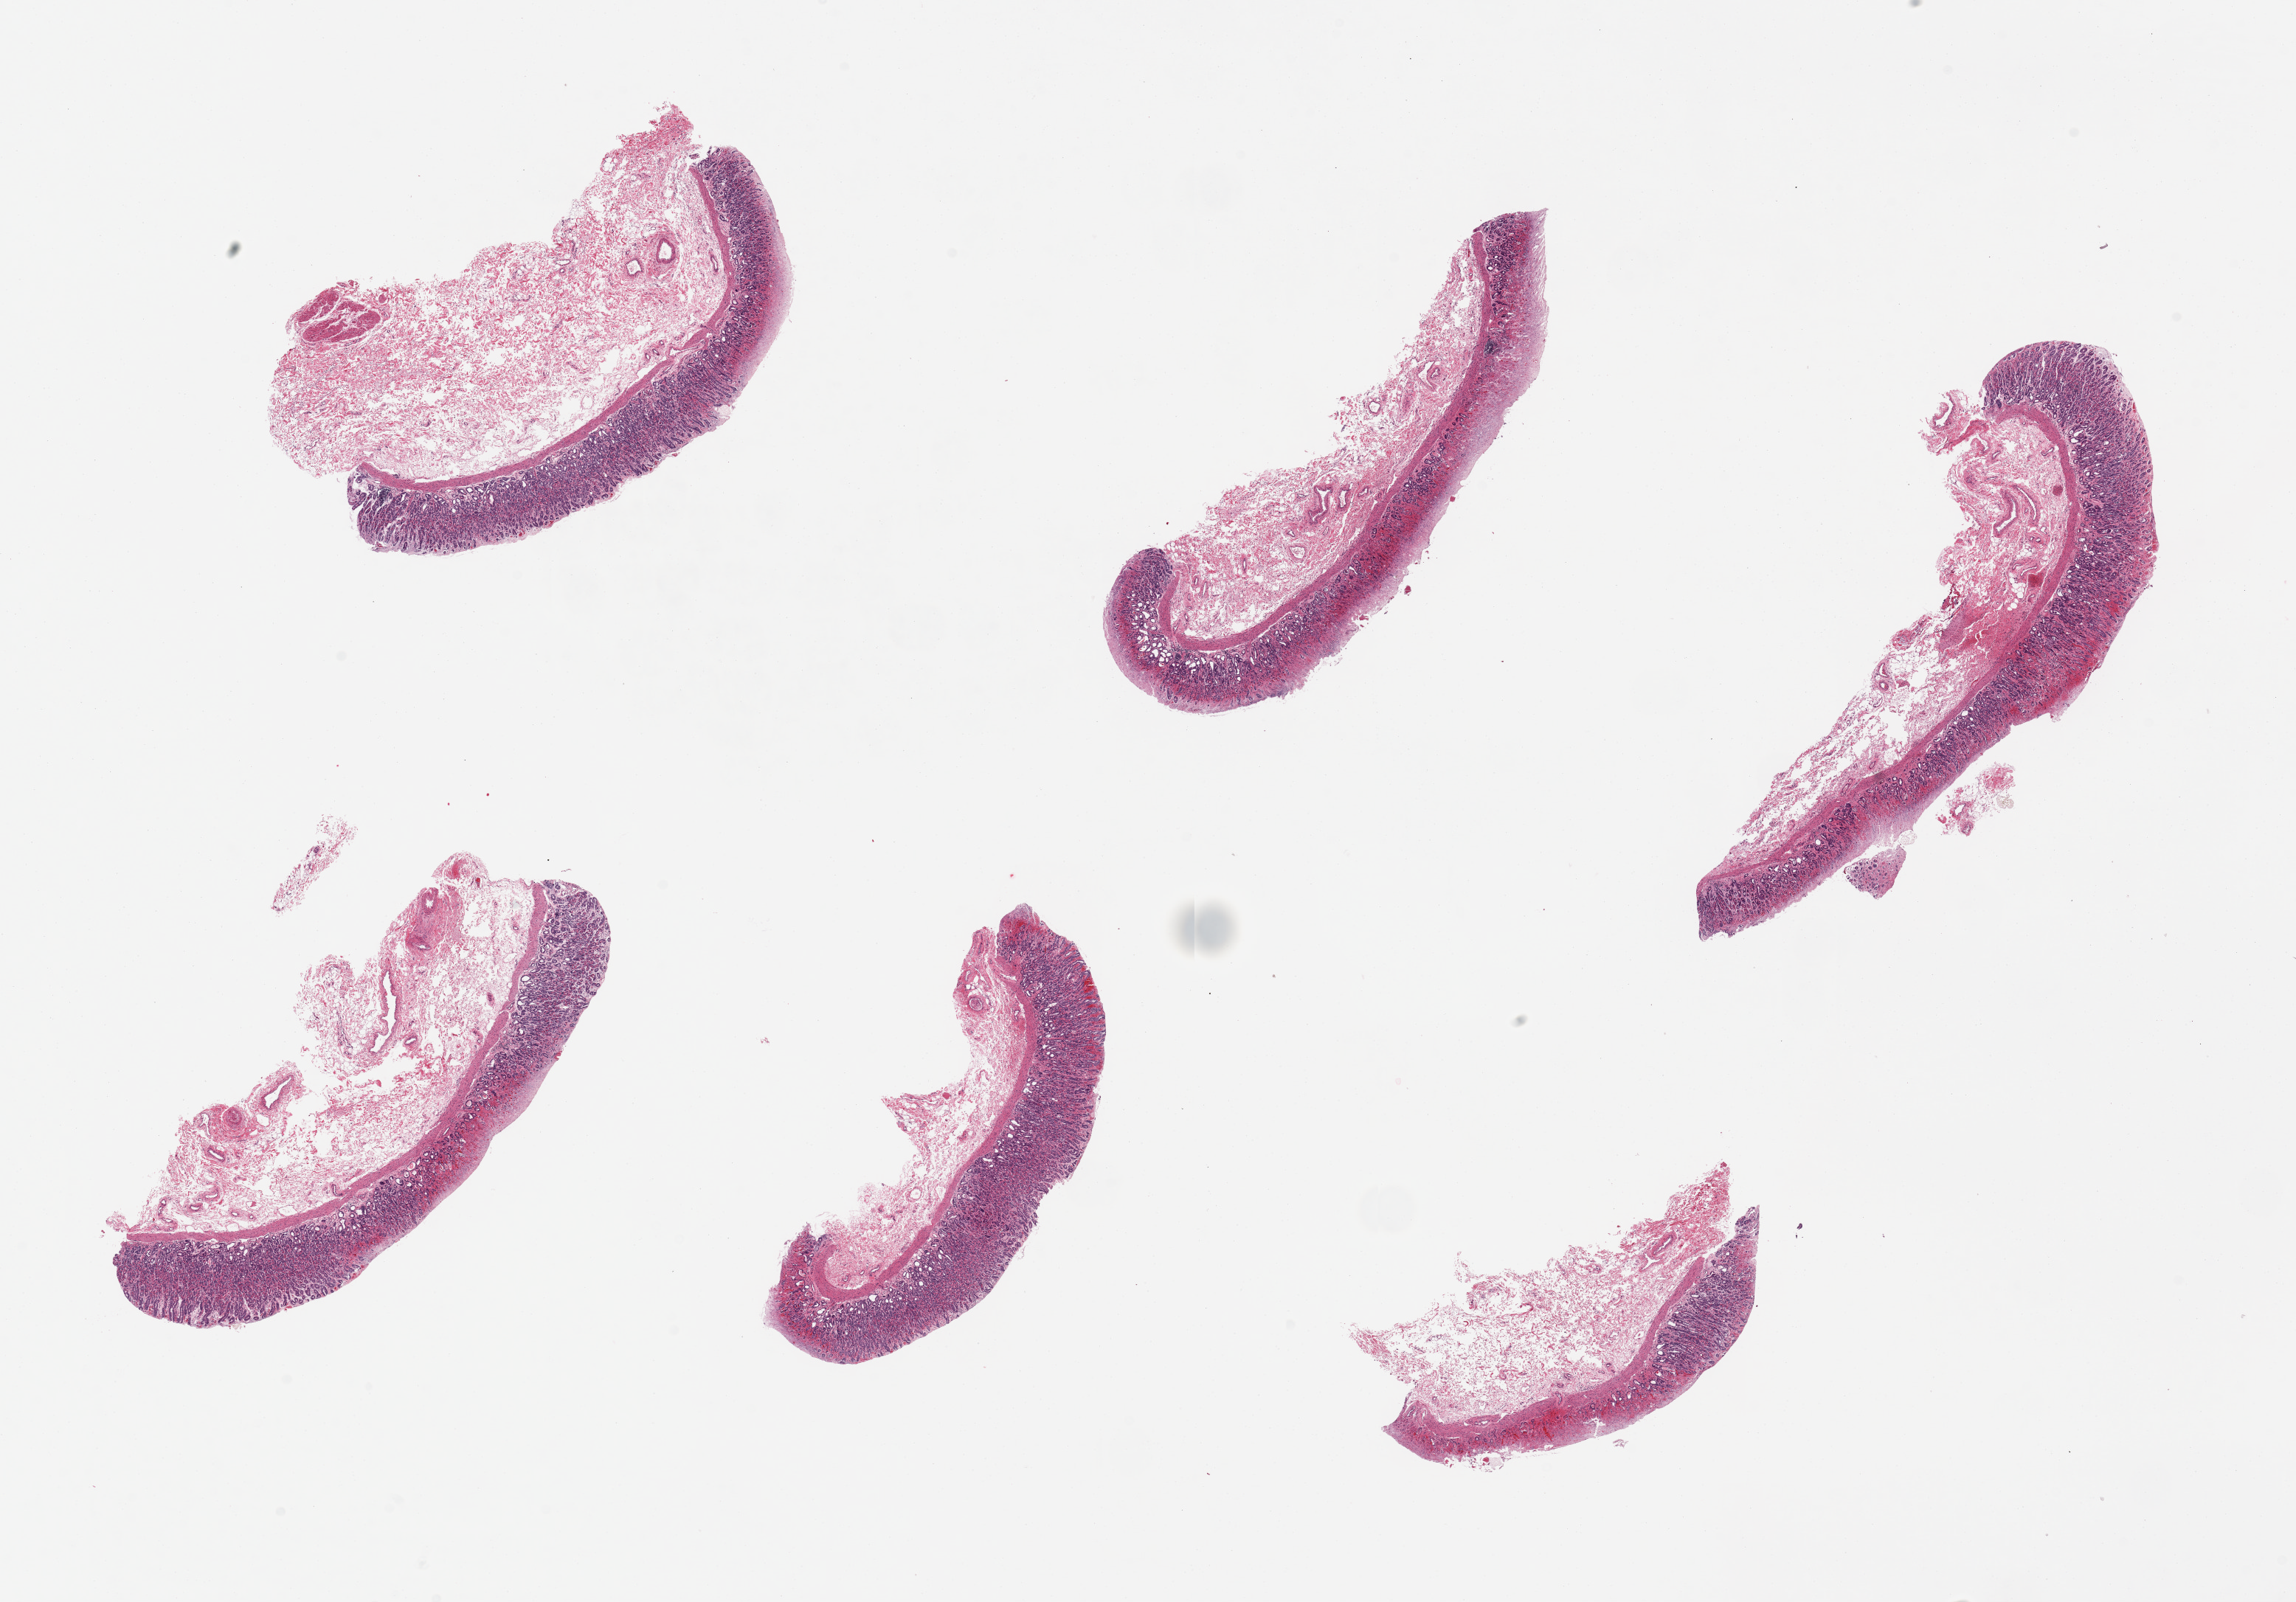
Haematoxylin and eosin whole-slide image — low-resolution overview of the scanned area, about 24.6 x 17.2 mm; PAXgene-fixed, paraffin-embedded tissue; sampled site (target tissue): stomach; donor tissue sample. Female donor.
• review note (as recorded): 6 pieces. up to 8x3mm; Mucosa and submucosa only